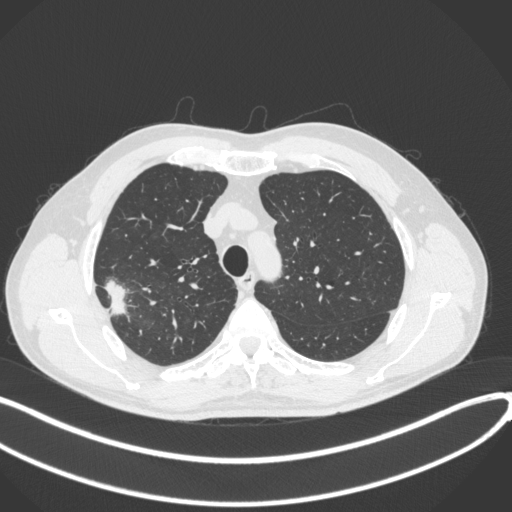
Chest CT, one axial slice. Position 324 of 381 along the scan axis. 120 kVp. Lung window (W 1500 / L -600 HU). 512 × 512 image matrix, field of view 400 × 400 mm. Patient: male, 62 years. Case-level facts recorded for this patient, not image findings: clinical TNM (as recorded): T1c N0 M0; histopathological grade: G2-3.
Outlined on this slice (rectangle marked by the reading radiologist):
- lung tumour (recorded histology: adenocarcinoma): box from (x=98, y=274) to (x=133, y=318) px